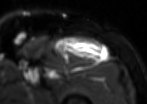
MRI of an extremity soft-tissue mass, one axial slice; position 74 of 85 along the scan axis; T2-weighted fat-saturated; MR volume resampled by the dataset authors to the PET/CT grid (not the native acquisition matrix); 3.27 mm slice thickness; 147 × 104 image matrix, field of view 144 × 102 mm. Male patient. From the clinical record (not read from this slice): histological type: extraskeletal osteosarcoma; grade: high; site of the primary tumour: thigh.
Outlined on this slice (expert contour drawn on MRI and transferred to this co-registered scan by the dataset authors):
- gross tumour volume (mass): bounding box [x1, y1, x2, y2] px = [56, 35, 107, 61]